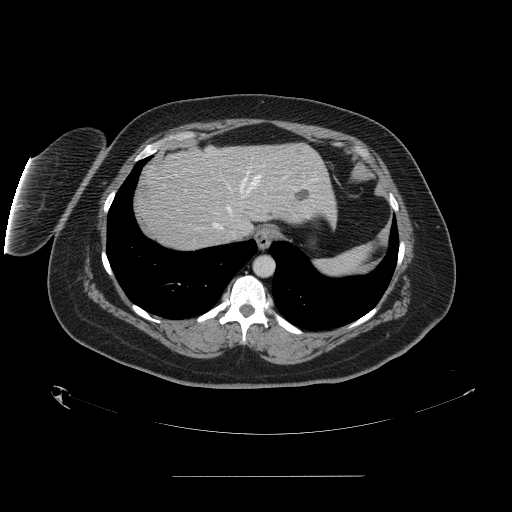
Contrast-enhanced abdominal CT, one axial slice. Slice 130 of 164 in the series (ordered by position). 120 kVp. Soft-tissue window (W 400 / L 40 HU). 512 × 512 image matrix, field of view 495 × 495 mm. Female patient, age 52 years. Case-level facts recorded for this patient, not image findings: diagnosis: colorectal cancer liver metastases, imaged before liver resection; multiple liver metastases: yes; largest metastasis: 3.5 cm; chemotherapy before resection: no.
Structures marked on this image (expert manual segmentation):
- hepatic veins: bounding box [x1, y1, x2, y2] px = [213, 172, 287, 238]
- liver: [139, 144, 335, 252]
- planned liver remnant (the part of the liver to remain after resection): [173, 144, 335, 230]
- liver metastasis: [296, 190, 310, 202]
- liver metastasis: [268, 210, 274, 218]